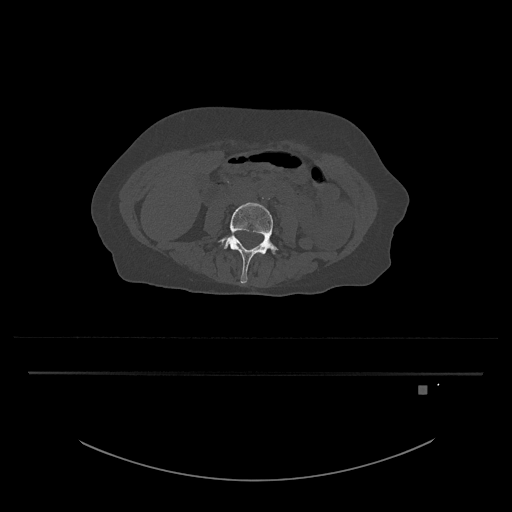
CT including the spine, one axial slice; position 363 of 797 along the scan axis; reconstruction kernel Br40s/3; bone window (W 1800 / L 400 HU); 0.5 mm slice thickness; 512 × 512 image matrix, field of view 500 × 500 mm. Female patient, age 57 years. Case-level facts recorded for this patient, not image findings: primary cancer: cervical.
Structures marked on this image (semi-automatically segmented with operator editing):
- L4 vertebra: bounding box (x1, y1, x2, y2) in pixels: (219, 202, 278, 284)